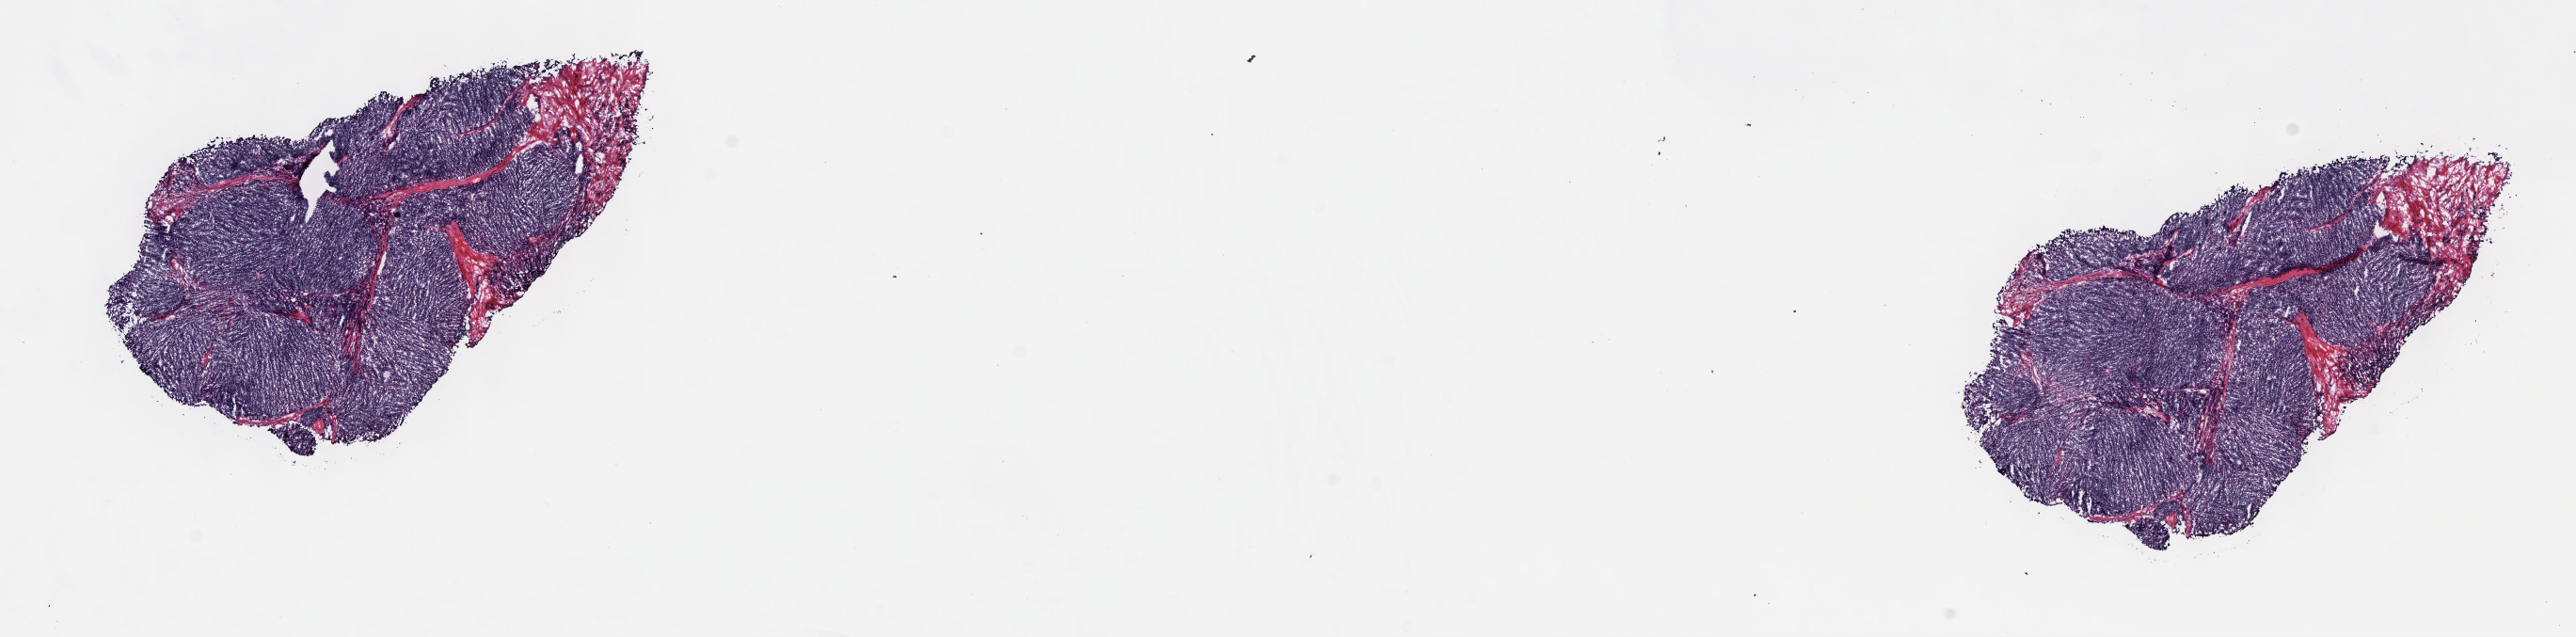
Digitized H&E-stained tissue section (whole slide) — a low-resolution overview of the entire scanned area, about 22.1 x 5.5 mm; frozen section from the top of the tissue portion; primary tumour sample from the thymus. Male, age 61 years at initial diagnosis. Slide review estimates, as recorded: tumour cells 100%, tumour nuclei 75%, normal cells 0%, stromal cells 0%, necrosis 0%. Inflammatory infiltration, as recorded: lymphocyte infiltration 2%, monocyte infiltration 0%, neutrophil infiltration 0%.
- histologic diagnosis: Thymoma, type AB, malignant